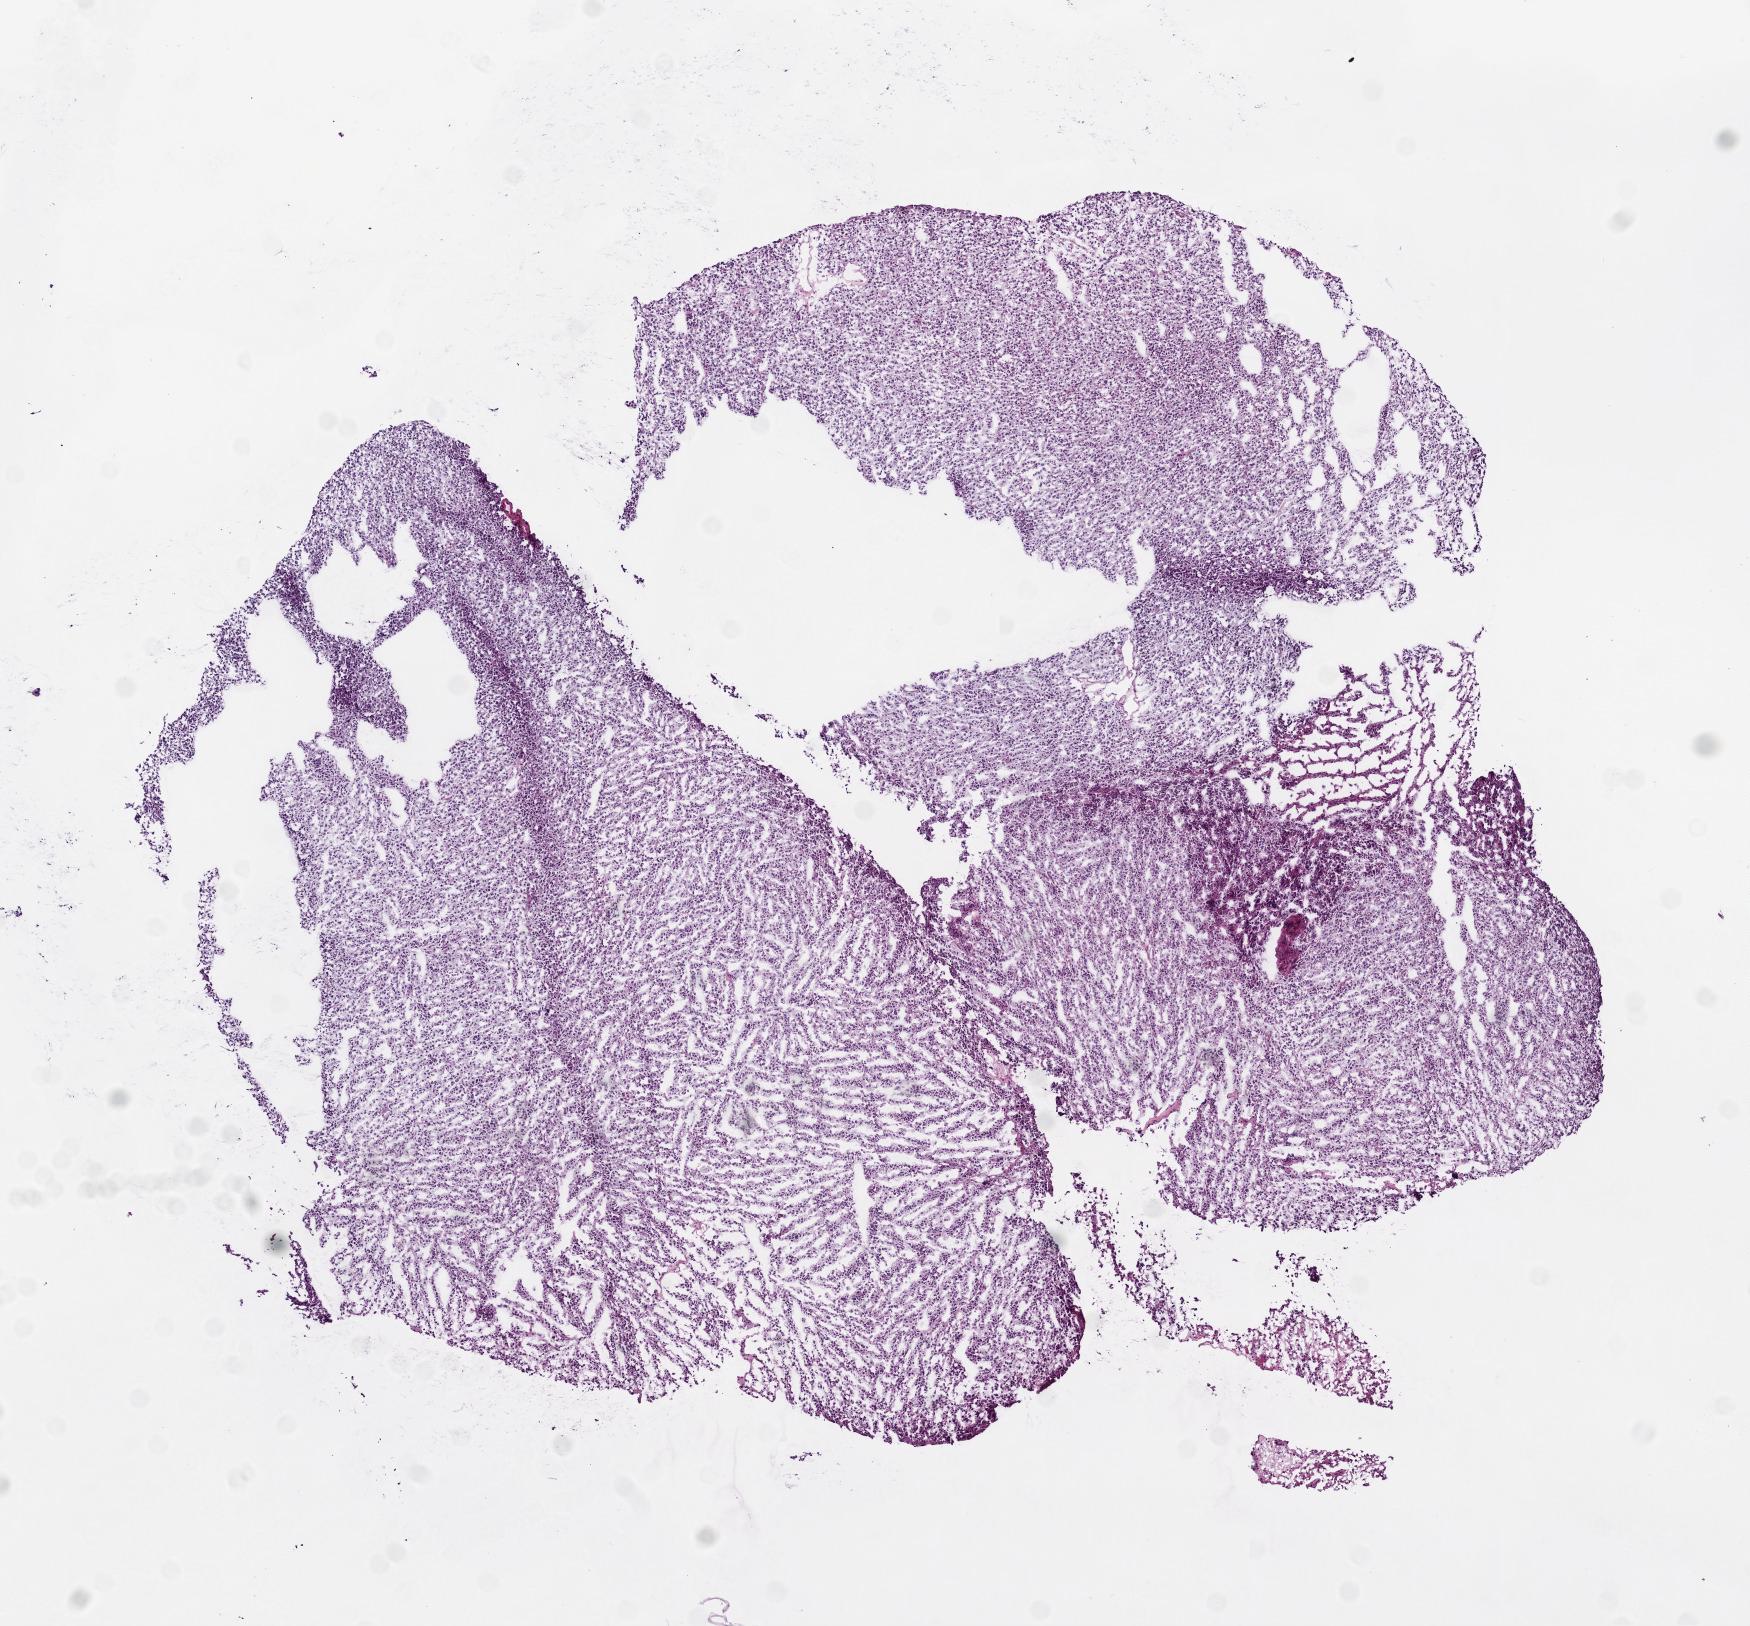
Whole-slide histology image, Hematoxylin and eosin (H&E) stained — whole scanned area (about 7.0 x 6.5 mm, slide scanned at 20x) shown as a low-resolution overview; frozen section from the bottom of the tissue portion; primary tumour sample from the brain. Female patient; age at initial diagnosis 42 years. Histologic grade: G2 (moderately differentiated). Composition of this section per pathologist review: tumour cells 100%, tumour nuclei 80%, normal cells 0%, stromal cells 0%, necrosis 0%.
• laterality: left
• histologic diagnosis: Oligodendroglioma, NOS